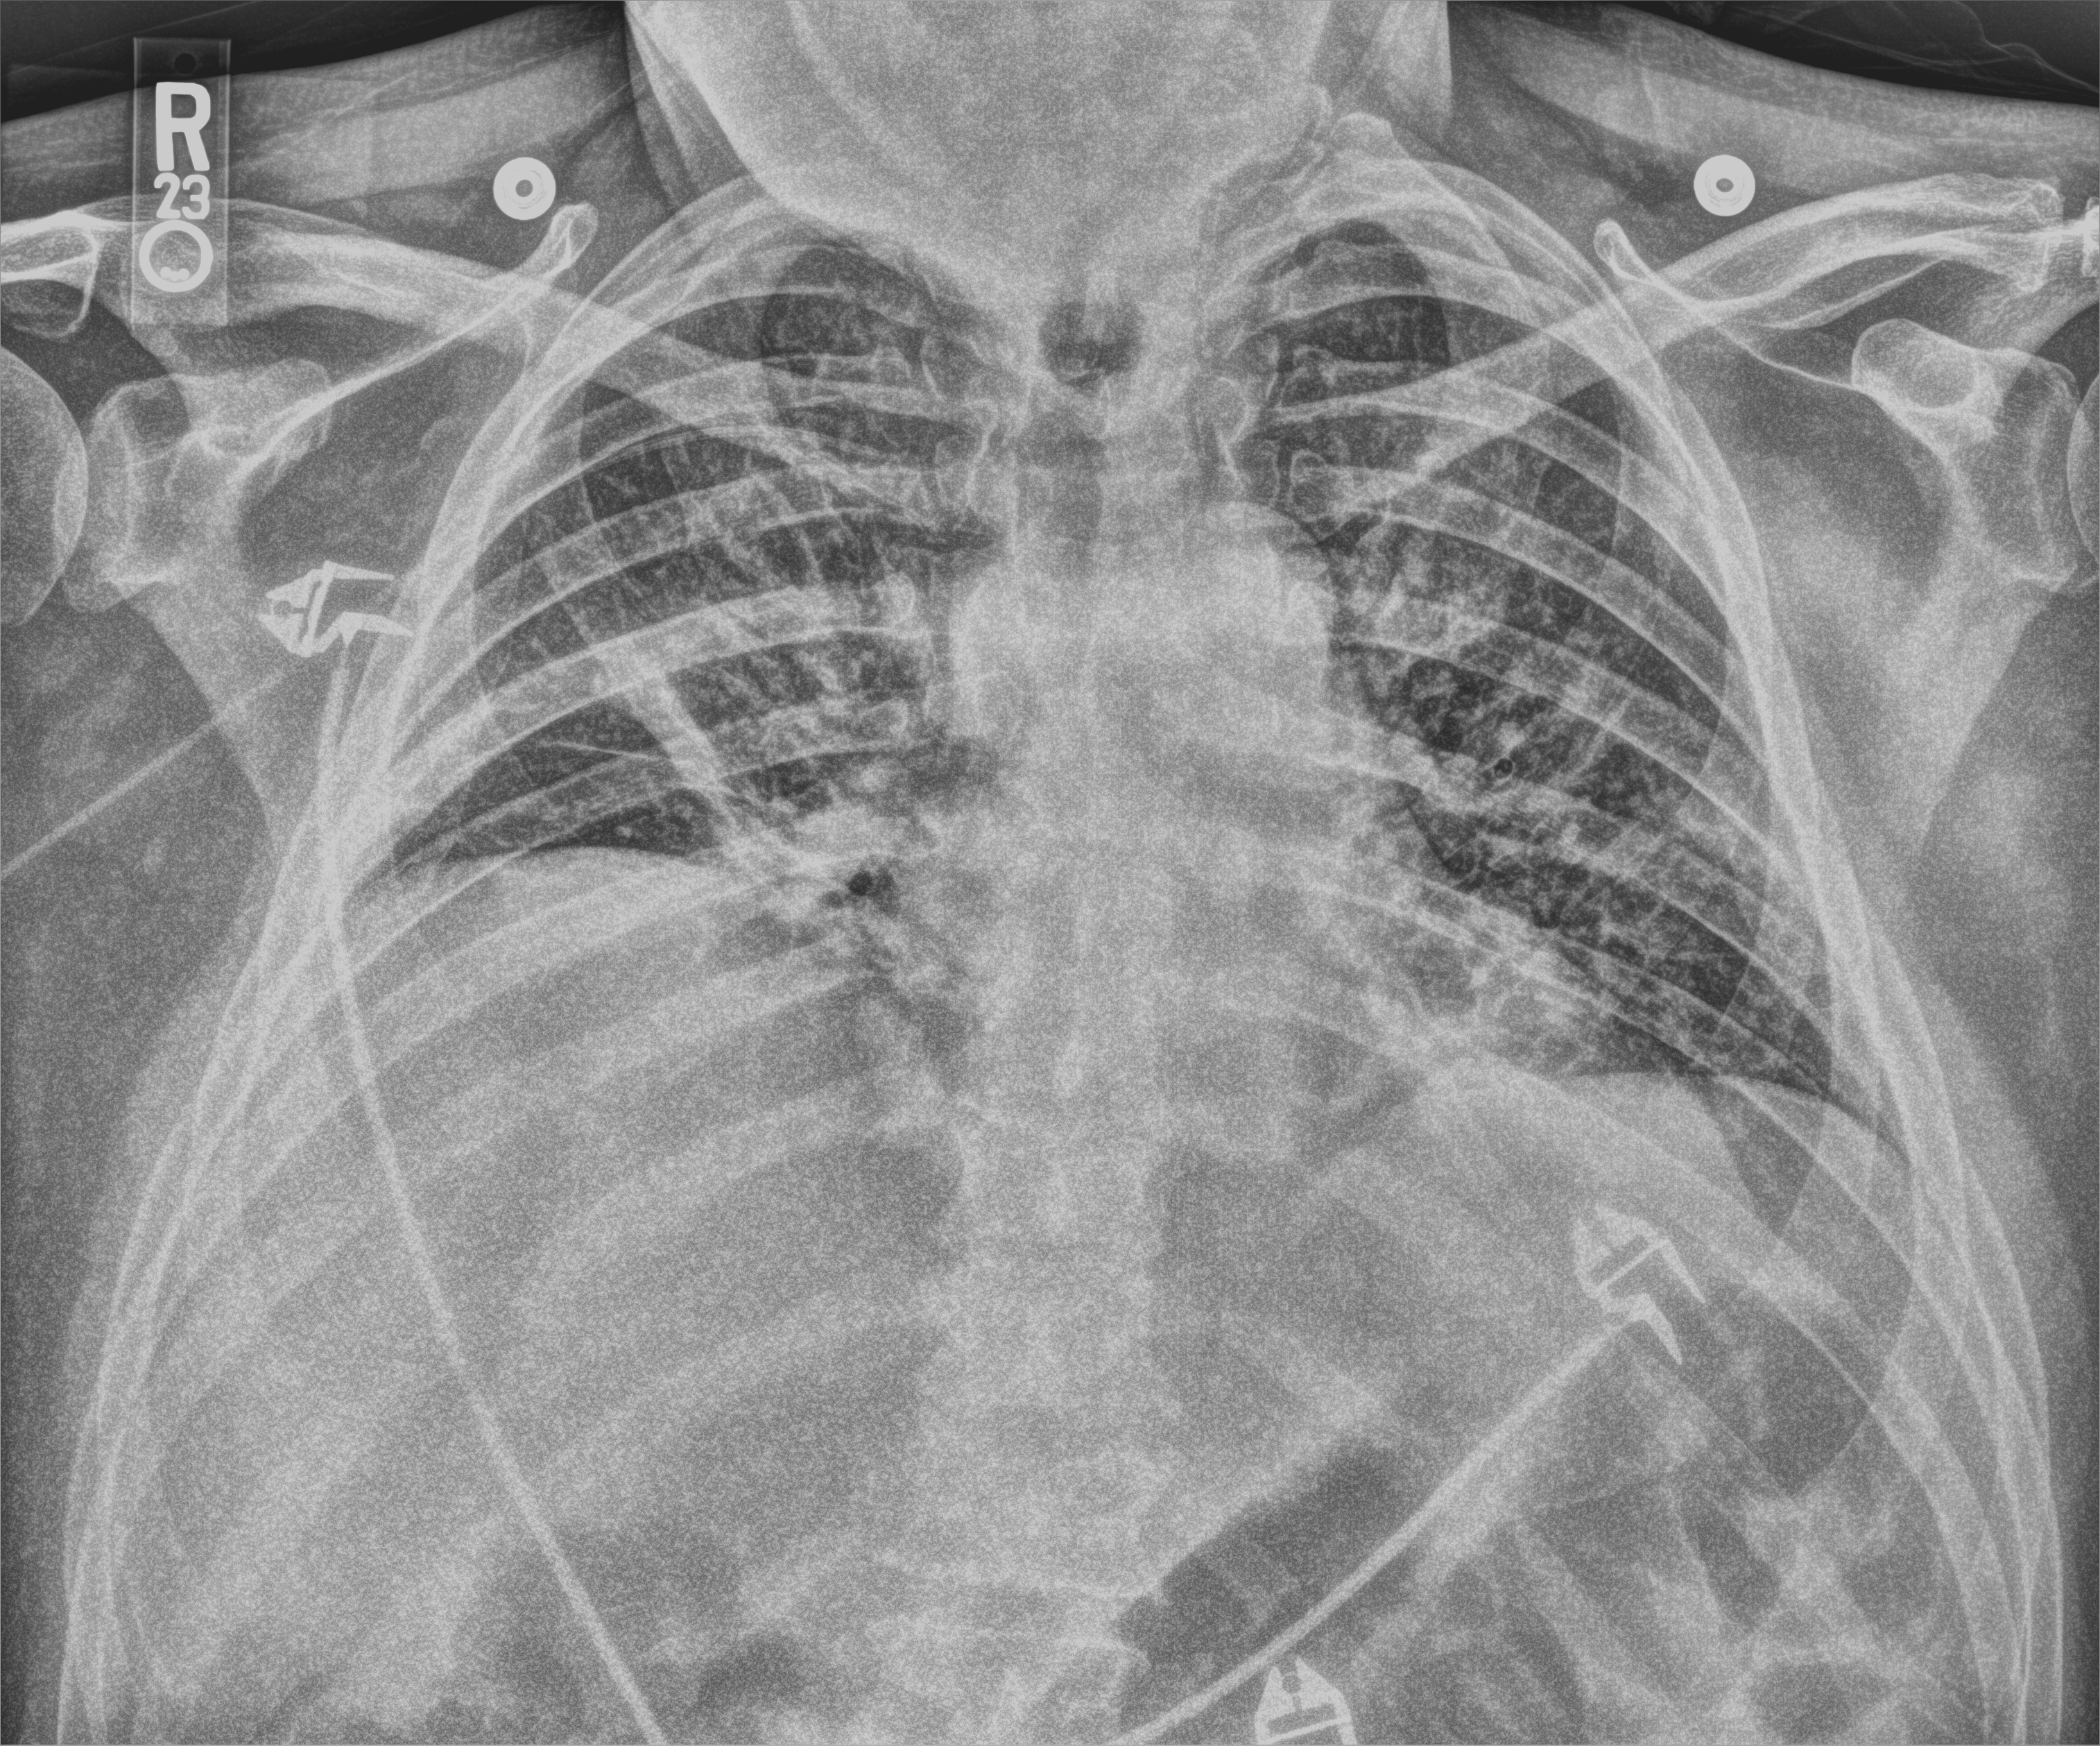
Portable chest radiograph; anteroposterior (AP) projection. Male patient hospitalised with COVID-19, age 18–59 years.
From the hospital-stay record, not from the radiograph (when in the stay this image was taken is not recorded): smoking status (admission record): never; admitted to intensive care during this hospital stay: yes; mechanically ventilated during this hospital stay: yes.